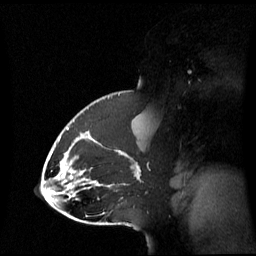
Breast MRI (dynamic contrast-enhanced), one sagittal slice; slice 39 of 60 in the series (ordered by position); dynamic contrast-enhanced series, image 2 of 3 at this slice position (ordered by acquisition); 1.5 T; TE 4.2 ms, TR 8.4 ms; 2.8 mm slice thickness; 256 × 256 image matrix, field of view 270 × 270 mm. Patient: female, 43 years. From the clinical record (not read from this slice): setting: breast cancer imaged before/during neoadjuvant chemotherapy; receptor status: triple-negative.
Annotated regions visible in this slice (semi-automatic segmentation, software-assisted and operator-edited):
- analysis volume of interest (the breast-tissue region the enhancement analysis was run in; not a lesion): bounding box (x1, y1, x2, y2) in pixels: (65, 118, 143, 198)
- tumour enhancement mask (voxels above the 70 % enhancement threshold inside the analysis volume of interest): (67, 128, 120, 181)